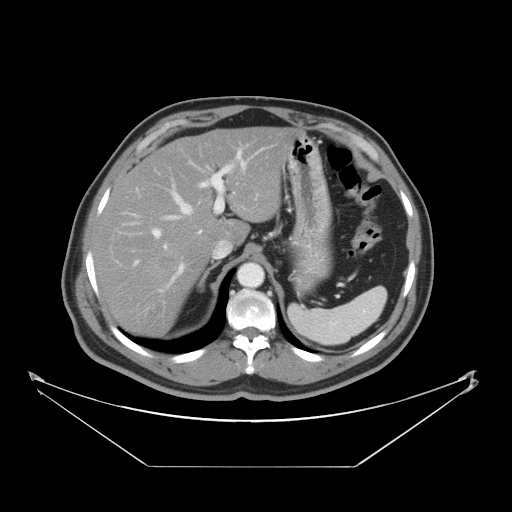
Contrast-enhanced abdominal CT, one axial slice. Position 32 of 46 along the scan axis. Reconstruction kernel STANDARD. 120 kVp. Soft-tissue window (W 400 / L 40 HU). 512 × 512 image matrix, field of view 465 × 465 mm. Male patient, age 57 years. Case-level facts recorded for this patient, not image findings: diagnosis: colorectal cancer liver metastases, imaged before liver resection; multiple liver metastases: no; largest metastasis: 3.3 cm; disease in both lobes: no.
Outlined on this slice (outlined manually by an expert reader):
- hepatic veins: box from (x=163, y=185) to (x=193, y=220) px
- liver: (x=94, y=127)–(x=293, y=337)
- planned liver remnant (the part of the liver to remain after resection): (x=94, y=127)–(x=293, y=329)
- portal vein (with intrahepatic branches): (x=131, y=150)–(x=246, y=293)
- liver metastasis: (x=157, y=256)–(x=177, y=271)